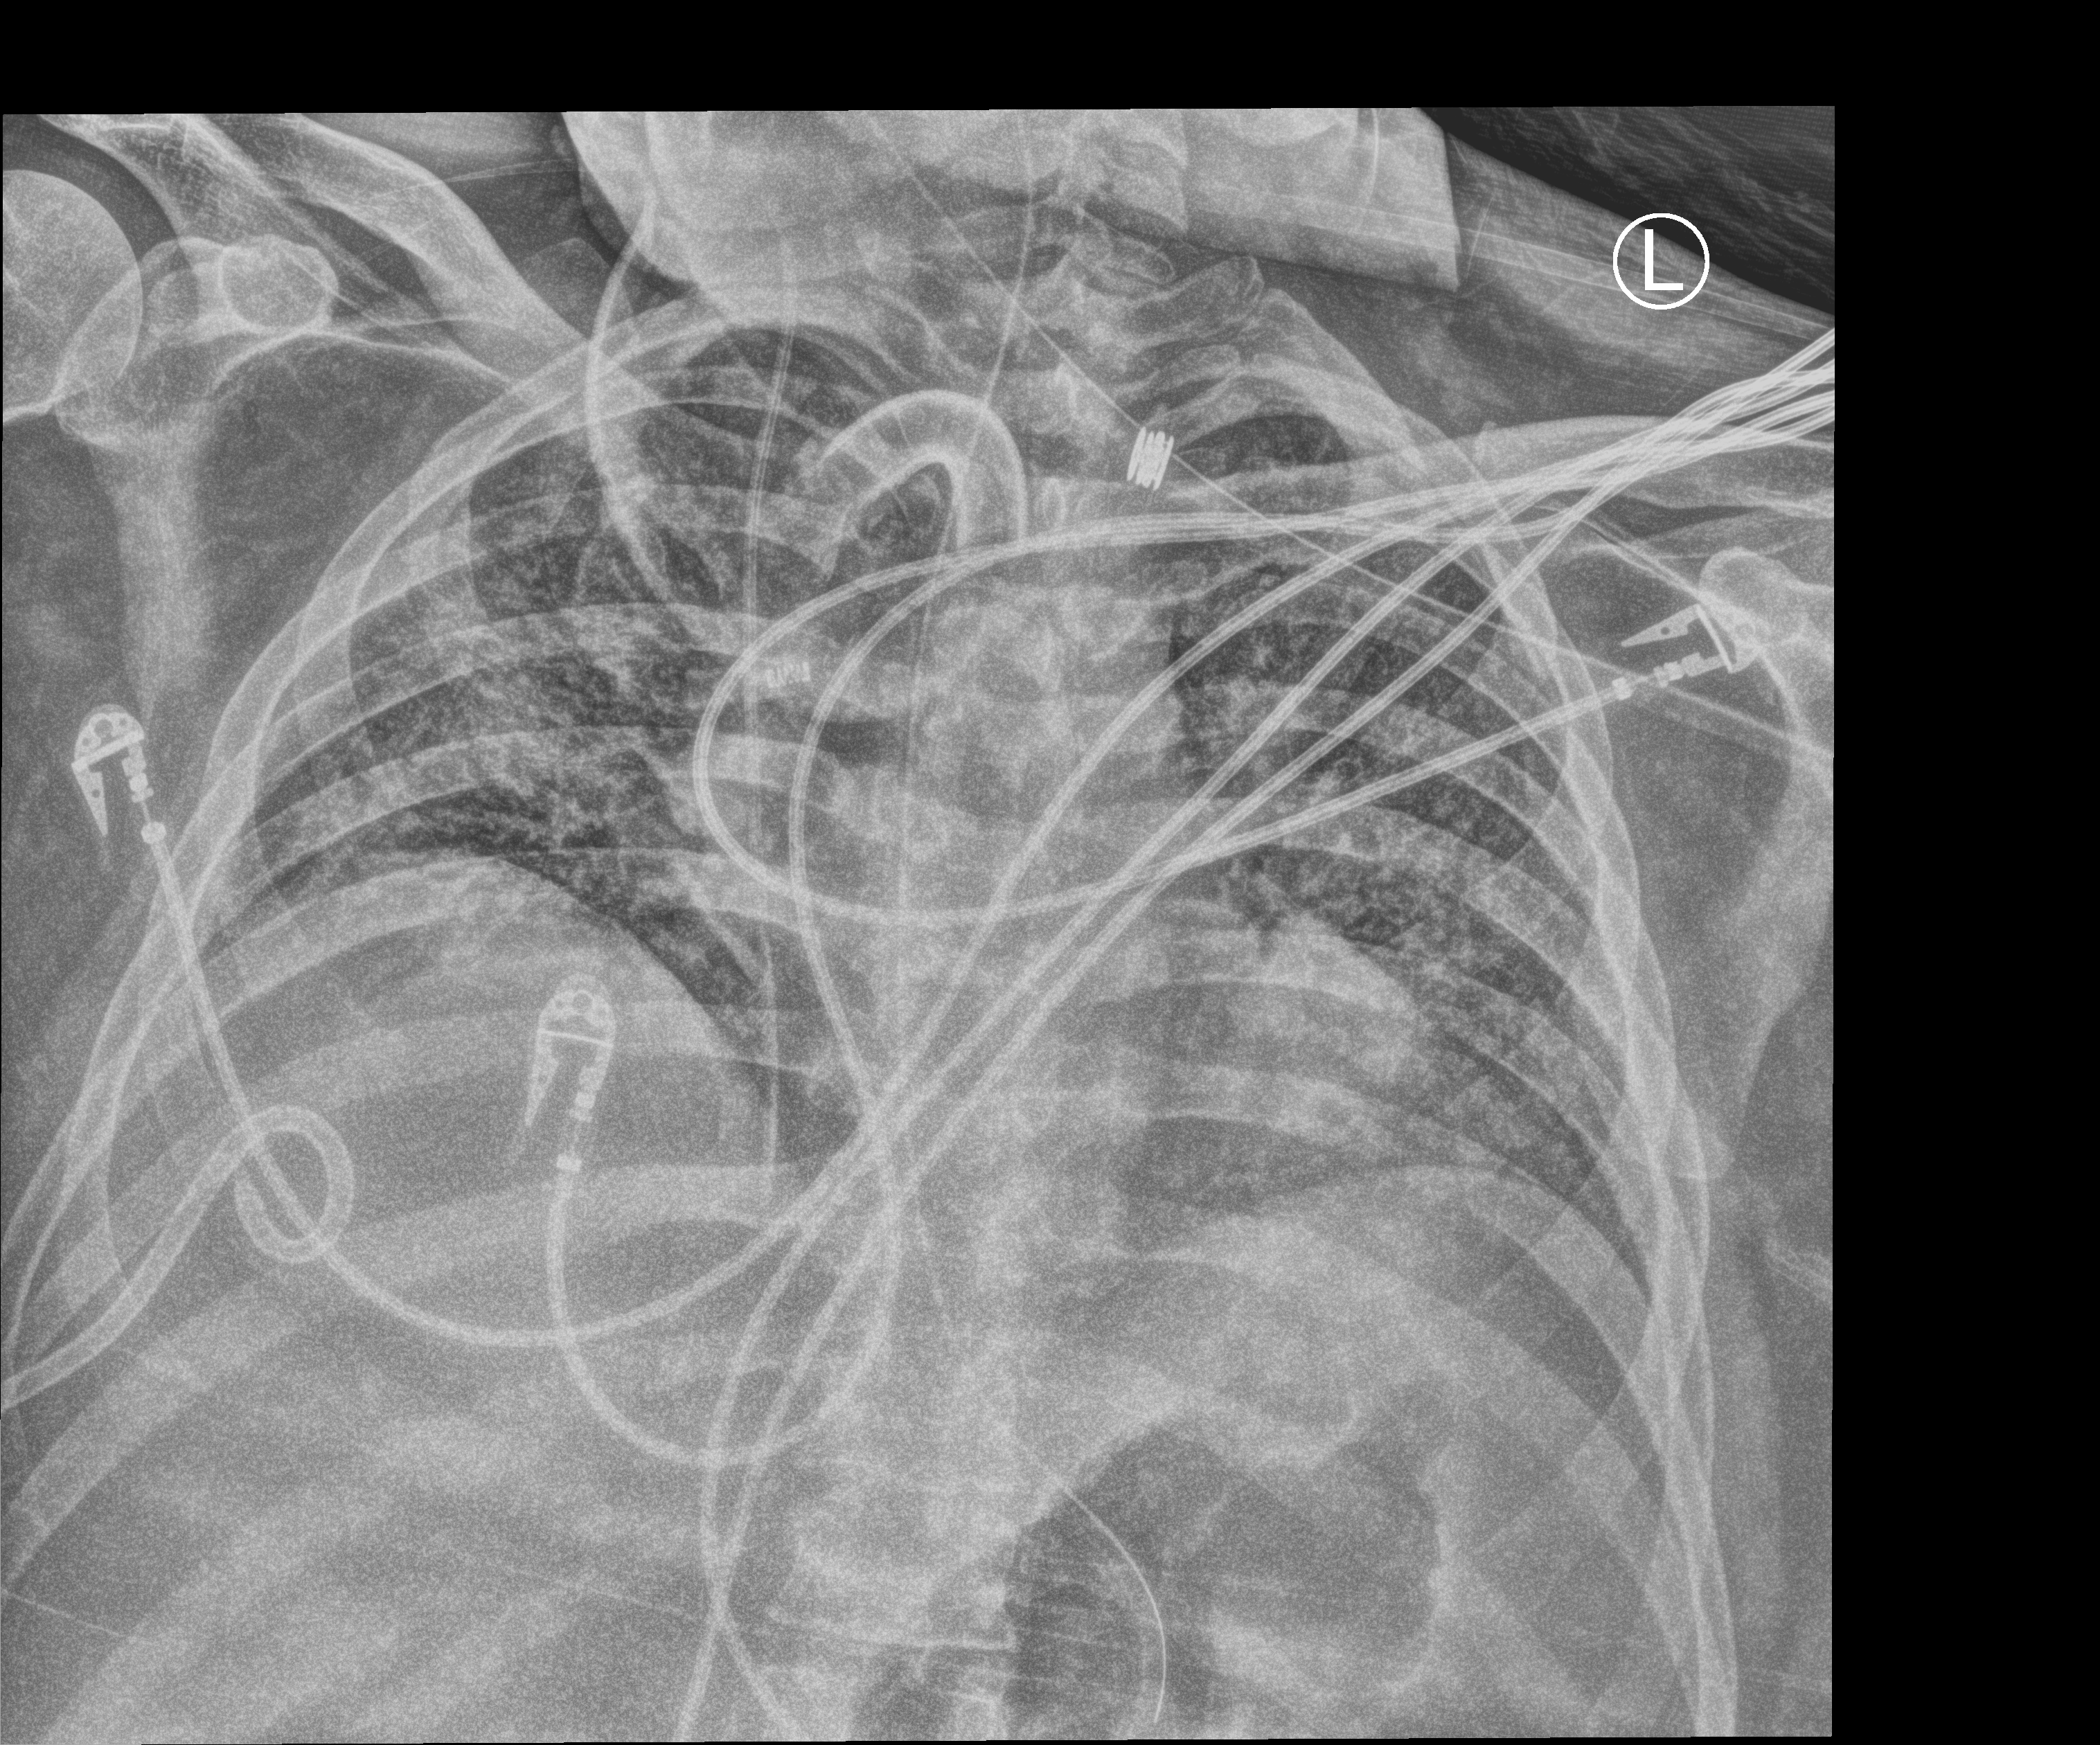
Portable chest radiograph; anteroposterior (AP) projection. Patient hospitalised with COVID-19; male, aged 18–59 years.
Admission-level facts for this patient (not findings on this image; timing relative to this image not recorded): mechanically ventilated during this hospital stay: yes; admitted to intensive care during this hospital stay: yes.